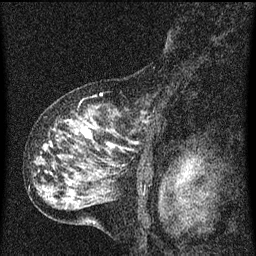
Breast MRI (dynamic contrast-enhanced), one sagittal slice. Dynamic contrast-enhanced series, image 2 of 3 at this slice position (ordered by acquisition). 1.5 T. TE 4.2 ms, TR 8 ms. 2 mm slice thickness. 256 × 256 image matrix. Female patient, age 55 years.
Structures marked on this image (semi-automatically segmented with operator editing):
- analysis volume of interest (the breast-tissue region the enhancement analysis was run in; not a lesion): box from (x=38, y=92) to (x=153, y=159) px
- tumour enhancement mask (voxels above the 70 % enhancement threshold inside the analysis volume of interest): (x=78, y=120)–(x=115, y=147)